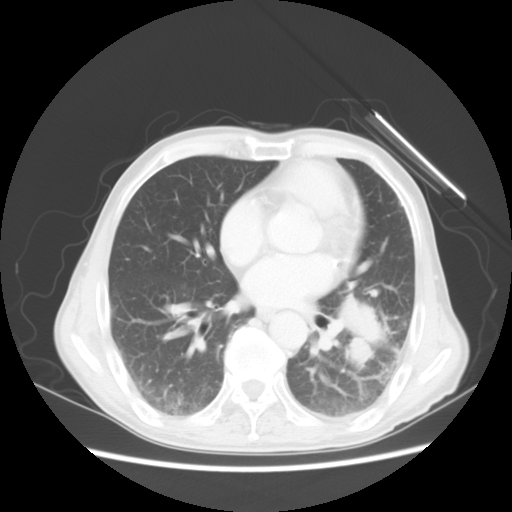
Chest CT, one axial slice; slice 23 of 51 in the series (ordered by position); 120 kVp; lung window (W 1500 / L -600 HU); 5 mm slice thickness; 512 × 512 image matrix, field of view 360 × 360 mm. Patient: male, 64 years. From the clinical record (not read from this slice): clinical TNM (as recorded): T4 N0 M0.
Outlined on this slice (bounding box drawn by a radiologist):
- lung tumour (recorded histology: squamous cell carcinoma): bounding box (x1, y1, x2, y2) in pixels: (334, 293, 385, 368)